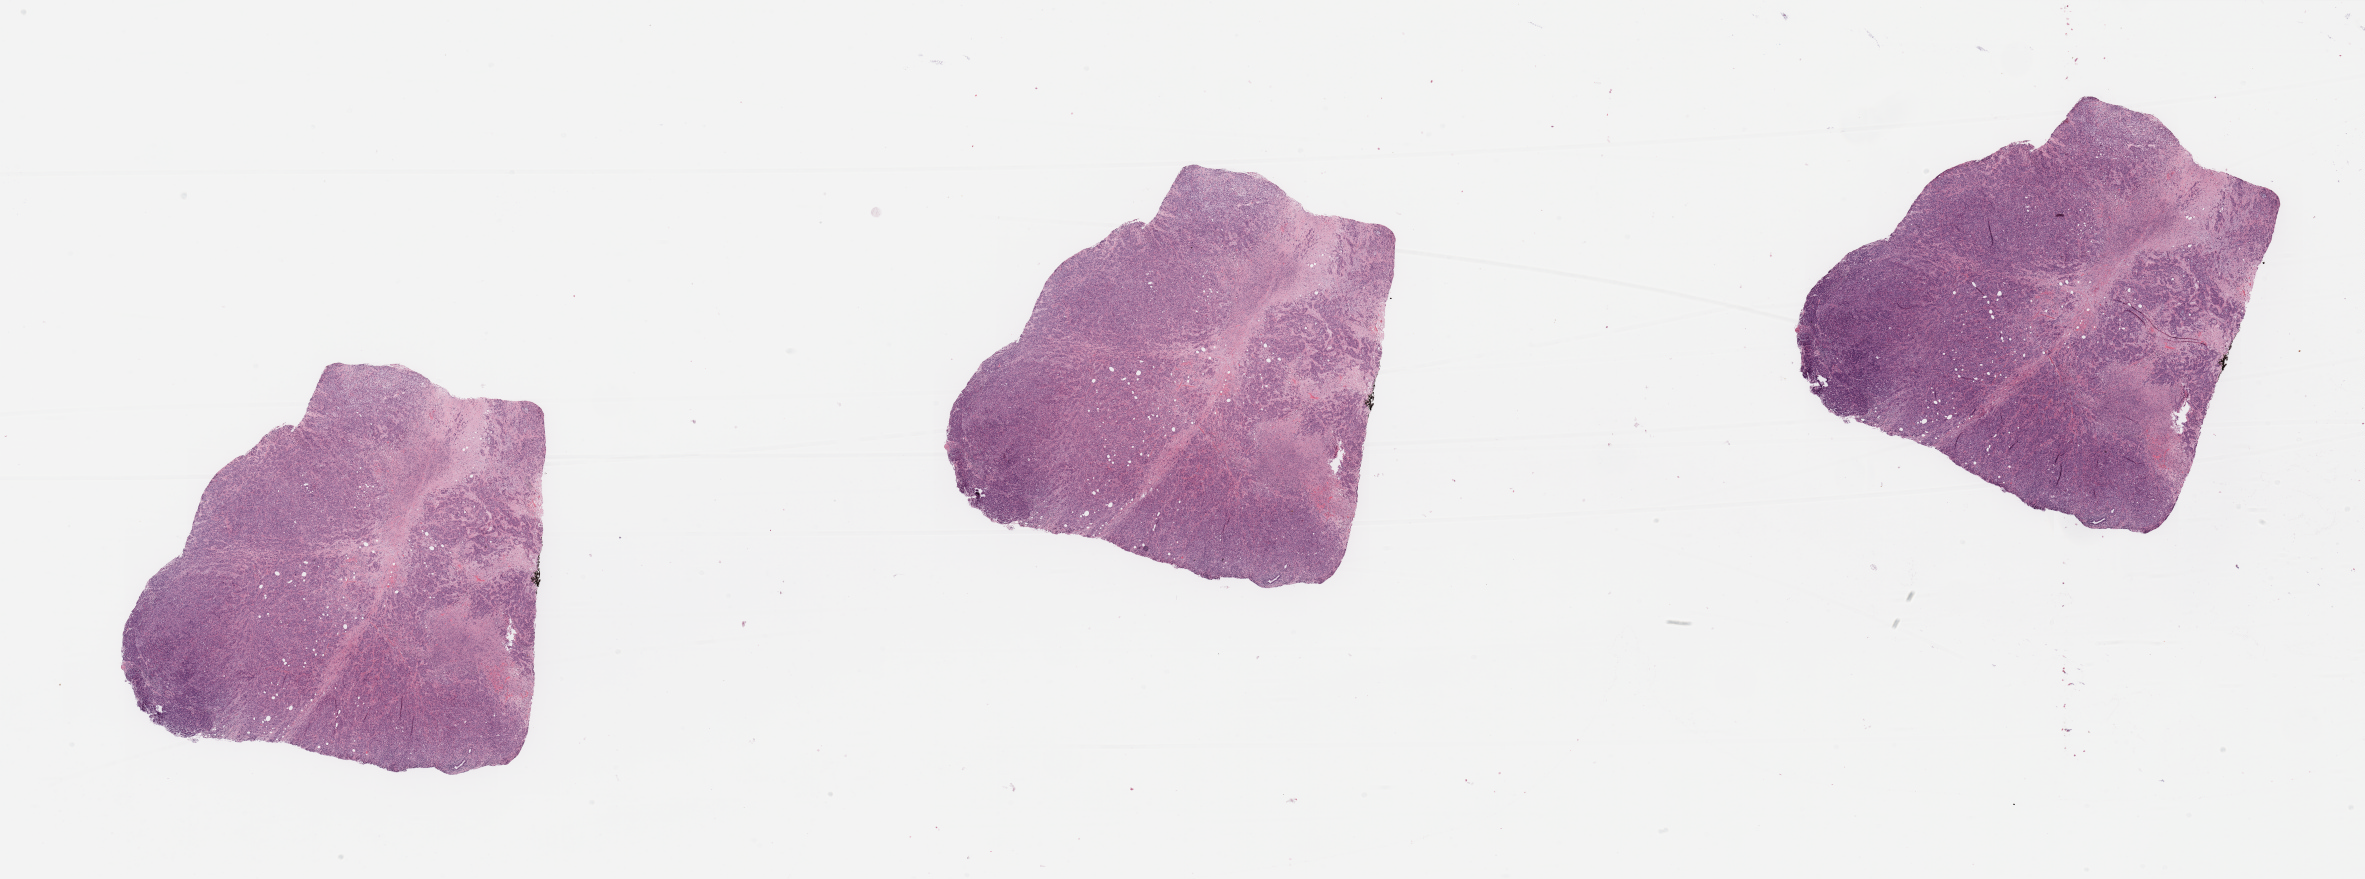
Digitized H&E tissue section (whole slide), shown as a low-resolution overview of the whole scanned area (about 37.4 x 13.9 mm, slide scanned at 20x), tumour tissue sample, sampled site: pancreas. Patient: male, age 76 years. Histologic grade: G3 (poorly differentiated). Composition of this section per pathologist review: tumour nuclei 50%, necrosis 20%.
* diagnosis: Infiltrating duct carcinoma, NOS
* AJCC pathologic stage: IB
* primary tumour site (as recorded): head